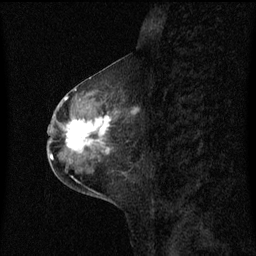
Breast MRI (dynamic contrast-enhanced), one sagittal slice; slice 28 of 60 in the series (ordered by position); dynamic contrast-enhanced series, image 2 of 3 at this slice position (ordered by acquisition); 1.5 T; TE 4.2 ms, TR 8.4 ms; 2 mm slice thickness; 256 × 256 image matrix, field of view 200 × 200 mm. Female patient, age 49 years. From the clinical record (not read from this slice): setting: breast cancer imaged before/during neoadjuvant chemotherapy; receptor status: HR-positive, HER2-negative.
Annotated regions visible in this slice (semi-automatic segmentation, software-assisted and operator-edited):
- analysis volume of interest (the breast-tissue region the enhancement analysis was run in; not a lesion): box from (x=59, y=101) to (x=130, y=158) px
- tumour enhancement mask (voxels above the 70 % enhancement threshold inside the analysis volume of interest): (x=67, y=115)–(x=112, y=153)